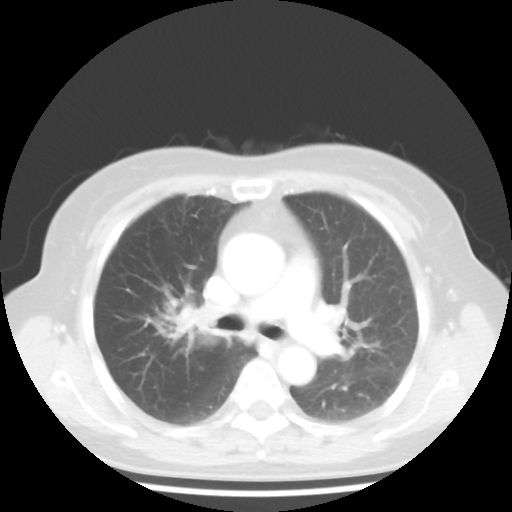
Chest CT, one axial slice; slice 27 of 44 in the series (ordered by position); lung window (W 1500 / L -600 HU); 512 × 512 image matrix, field of view 316 × 316 mm. Female patient, age 62 years. From the clinical record (not read from this slice): clinical TNM (as recorded): T3 N0 M0.
Annotated regions visible in this slice (bounding box drawn by a radiologist):
- lung tumour (recorded histology: small cell carcinoma): bounding box <161,295,208,344> (left, top, right, bottom; pixels)